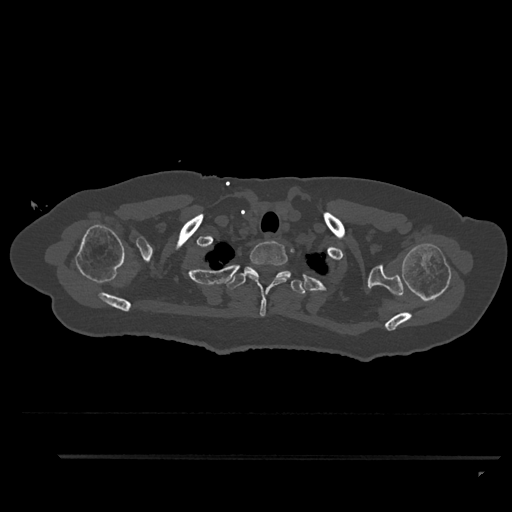
CT including the spine, one axial slice. Position 744 of 797 along the scan axis. Reconstruction kernel Br40s/3. 120 kVp. Bone window (W 1800 / L 400 HU). 0.5 mm slice thickness. 512 × 512 image matrix, field of view 408 × 408 mm. Patient: female, 44 years. From the clinical record (not read from this slice): primary cancer: renal; vertebrae with lytic lesions (as recorded): L1.
Annotated regions visible in this slice (semi-automatically segmented with operator editing):
- T1 vertebra: box from (x=247, y=240) to (x=288, y=317) px
- T2 vertebra: (x=227, y=267)–(x=306, y=294)